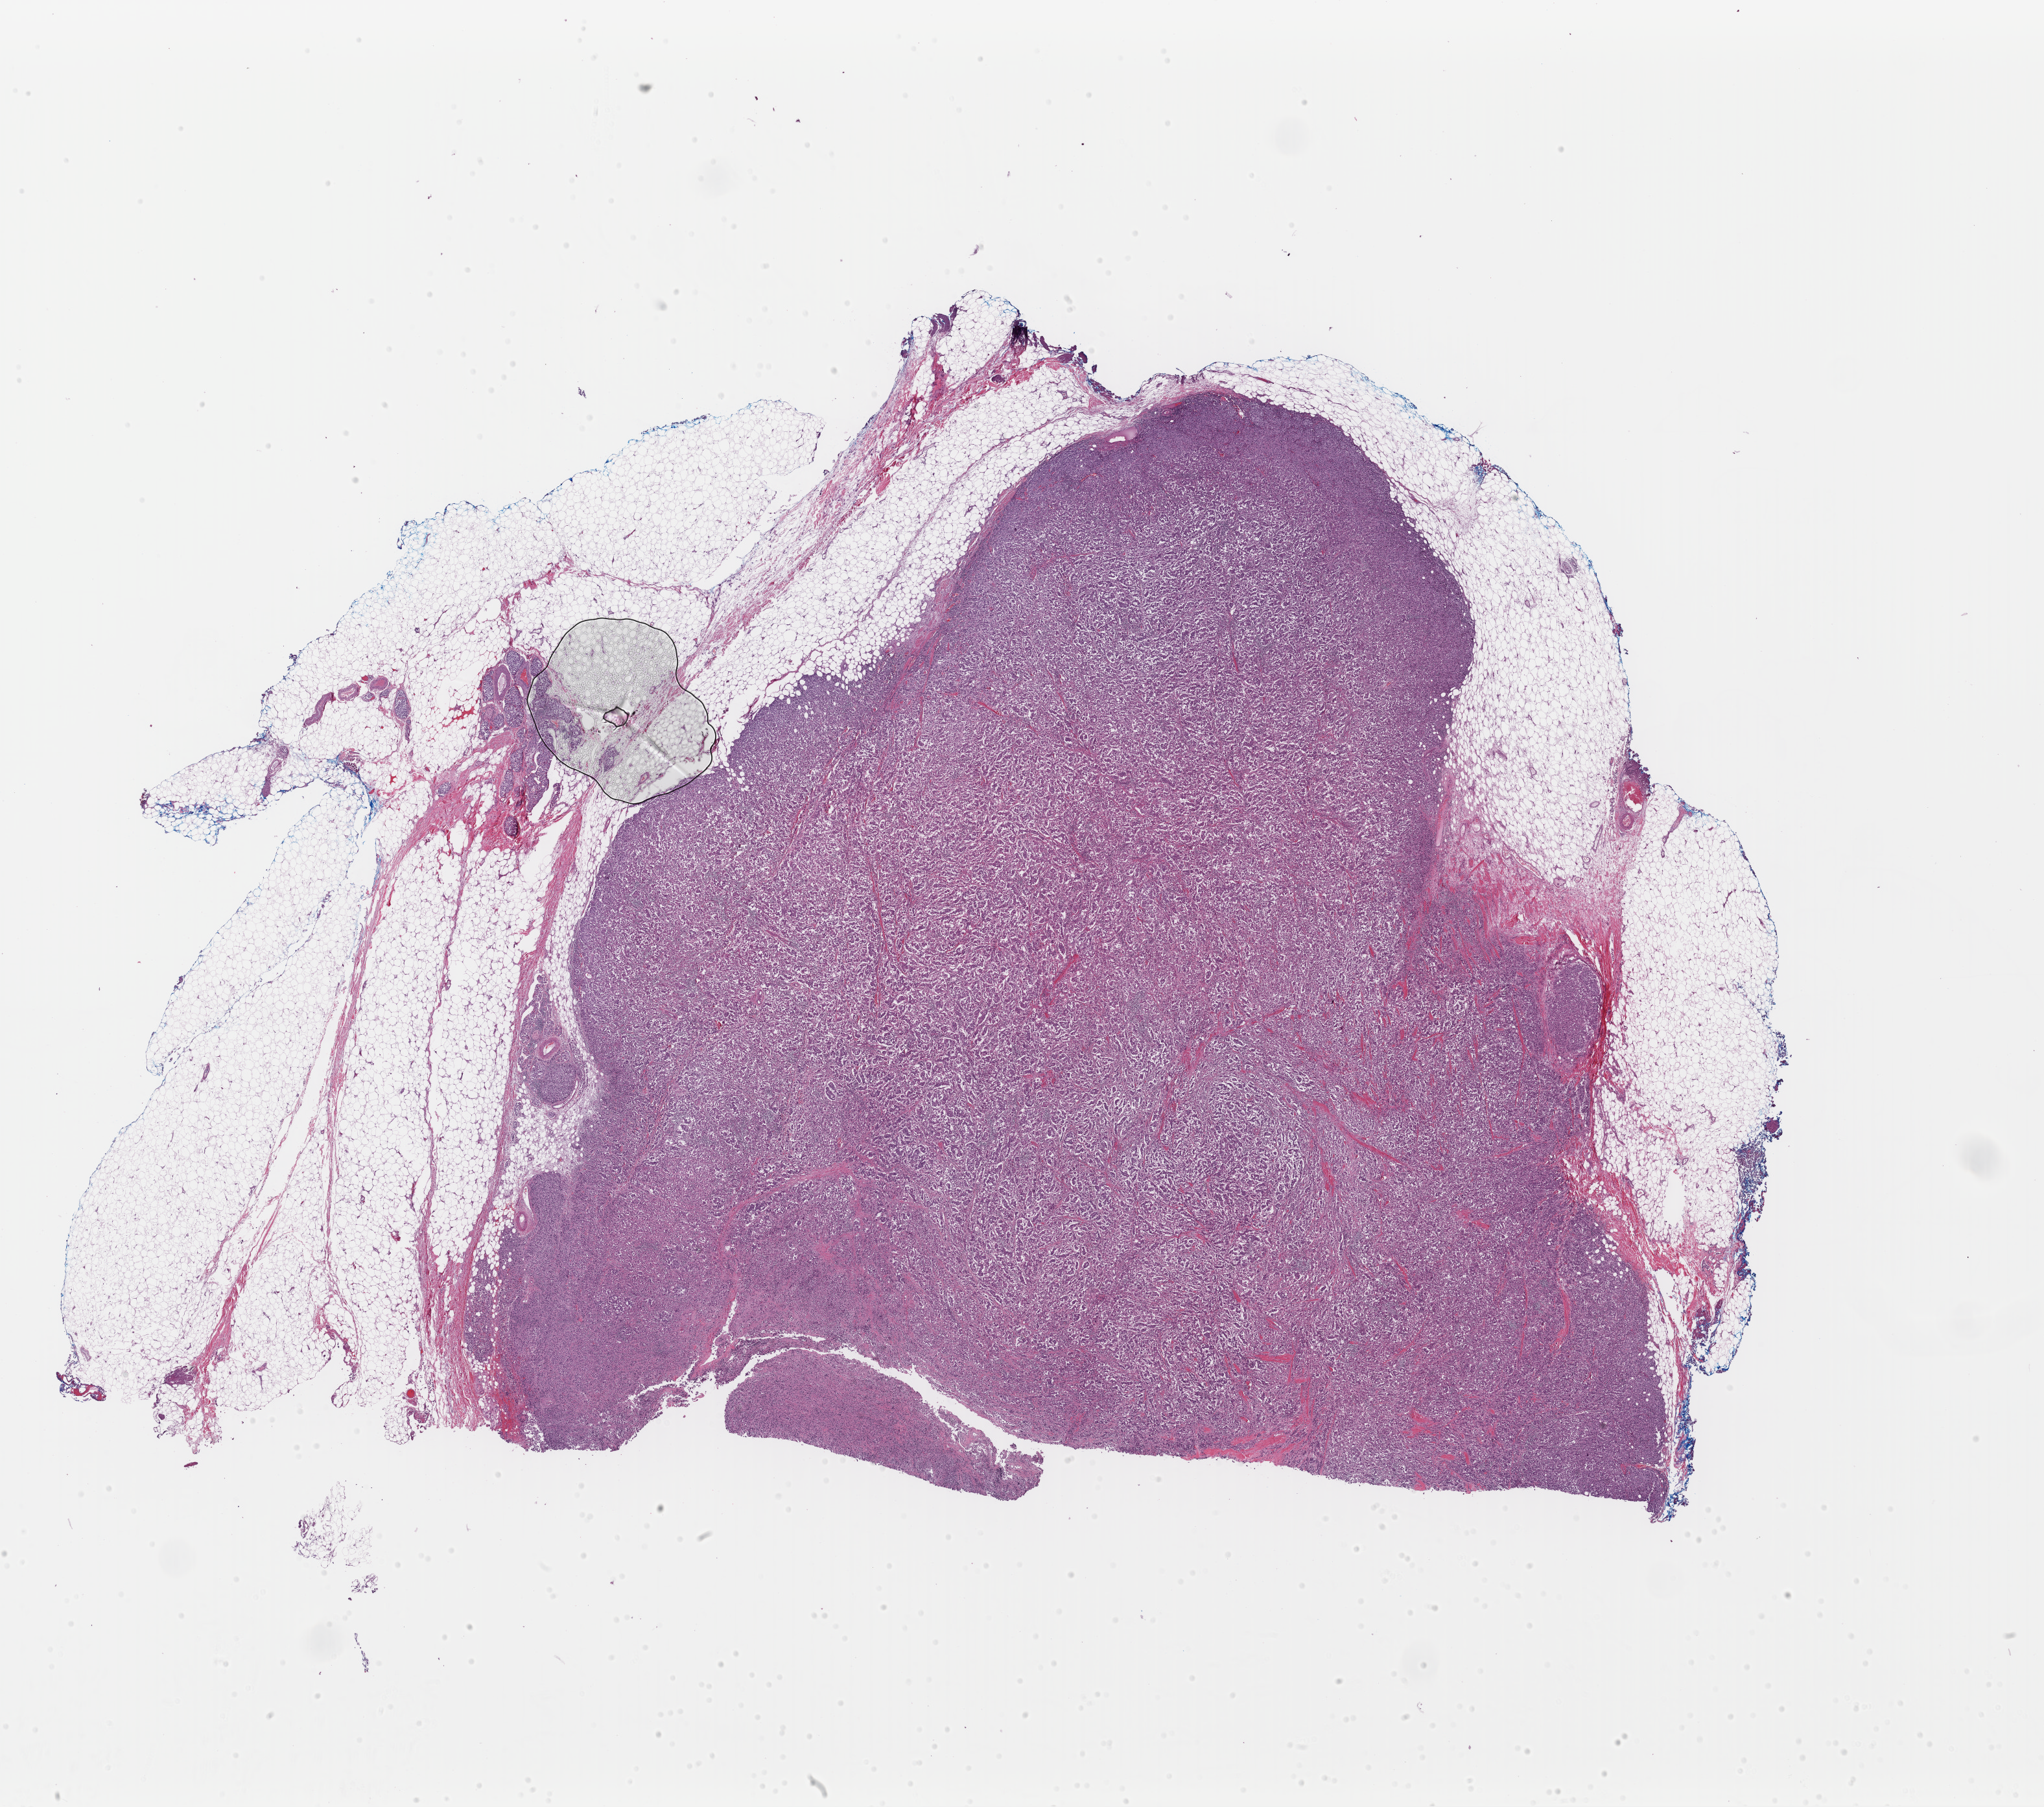
Hematoxylin and eosin (H&E) stained whole-slide image, whole scanned area (about 24.9 x 22.0 mm) shown as a low-resolution overview. FFPE section. Sample: primary tumour, skin. Male patient; age at initial diagnosis 30 years.
• diagnosis: Malignant melanoma, NOS